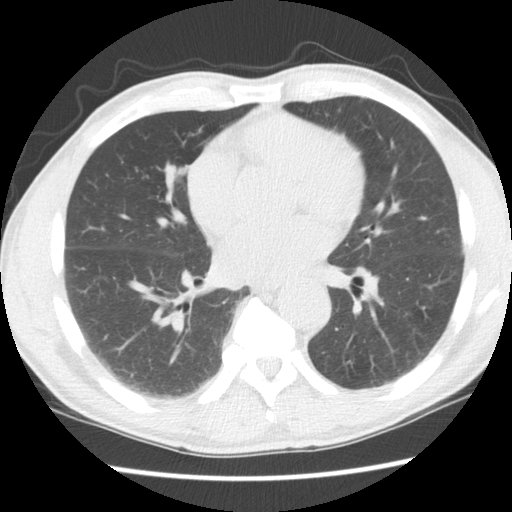
Chest CT (low-dose screening protocol), one axial image; second screening round (one year after baseline); lung window (W 1500 / L -600 HU); standard (soft-tissue) reconstruction kernel (STANDARD); 120 kVp; slice 83 of 152 in the series; 512 × 512 image matrix, field of view 337 × 337 mm. Male participant, aged 65 years at enrolment.
Expert-annotated lung lesion, bounding box (x1, y1, x2, y2) in pixels: (136, 155, 197, 209). Reader record for this screening exam (exam-level; its link to the box is not recorded): non-calcified nodule or mass ≥4 mm, right middle lobe, 11 × 9 mm, smooth margins, soft tissue attenuation, pre-existing on the prior screen: no. Official screen result: positive, other.